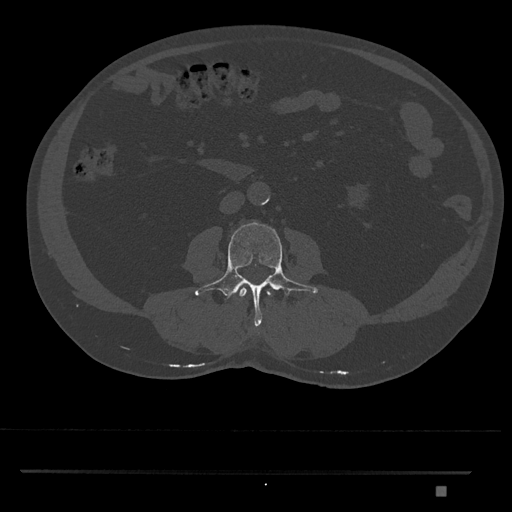
CT including the spine, one axial slice; position 687 of 1134 along the scan axis; reconstruction kernel Br40s/3; 120 kVp; bone window (W 1800 / L 400 HU); 0.5 mm slice thickness; 512 × 512 image matrix, field of view 429 × 429 mm. Patient: male, 65 years. From the clinical record (not read from this slice): primary cancer: prostate.
Annotated regions visible in this slice (semi-automatic segmentation, software-assisted and operator-edited):
- L2 vertebra: bounding box <238,285,272,299> (left, top, right, bottom; pixels)
- L3 vertebra: <195,222,318,327>